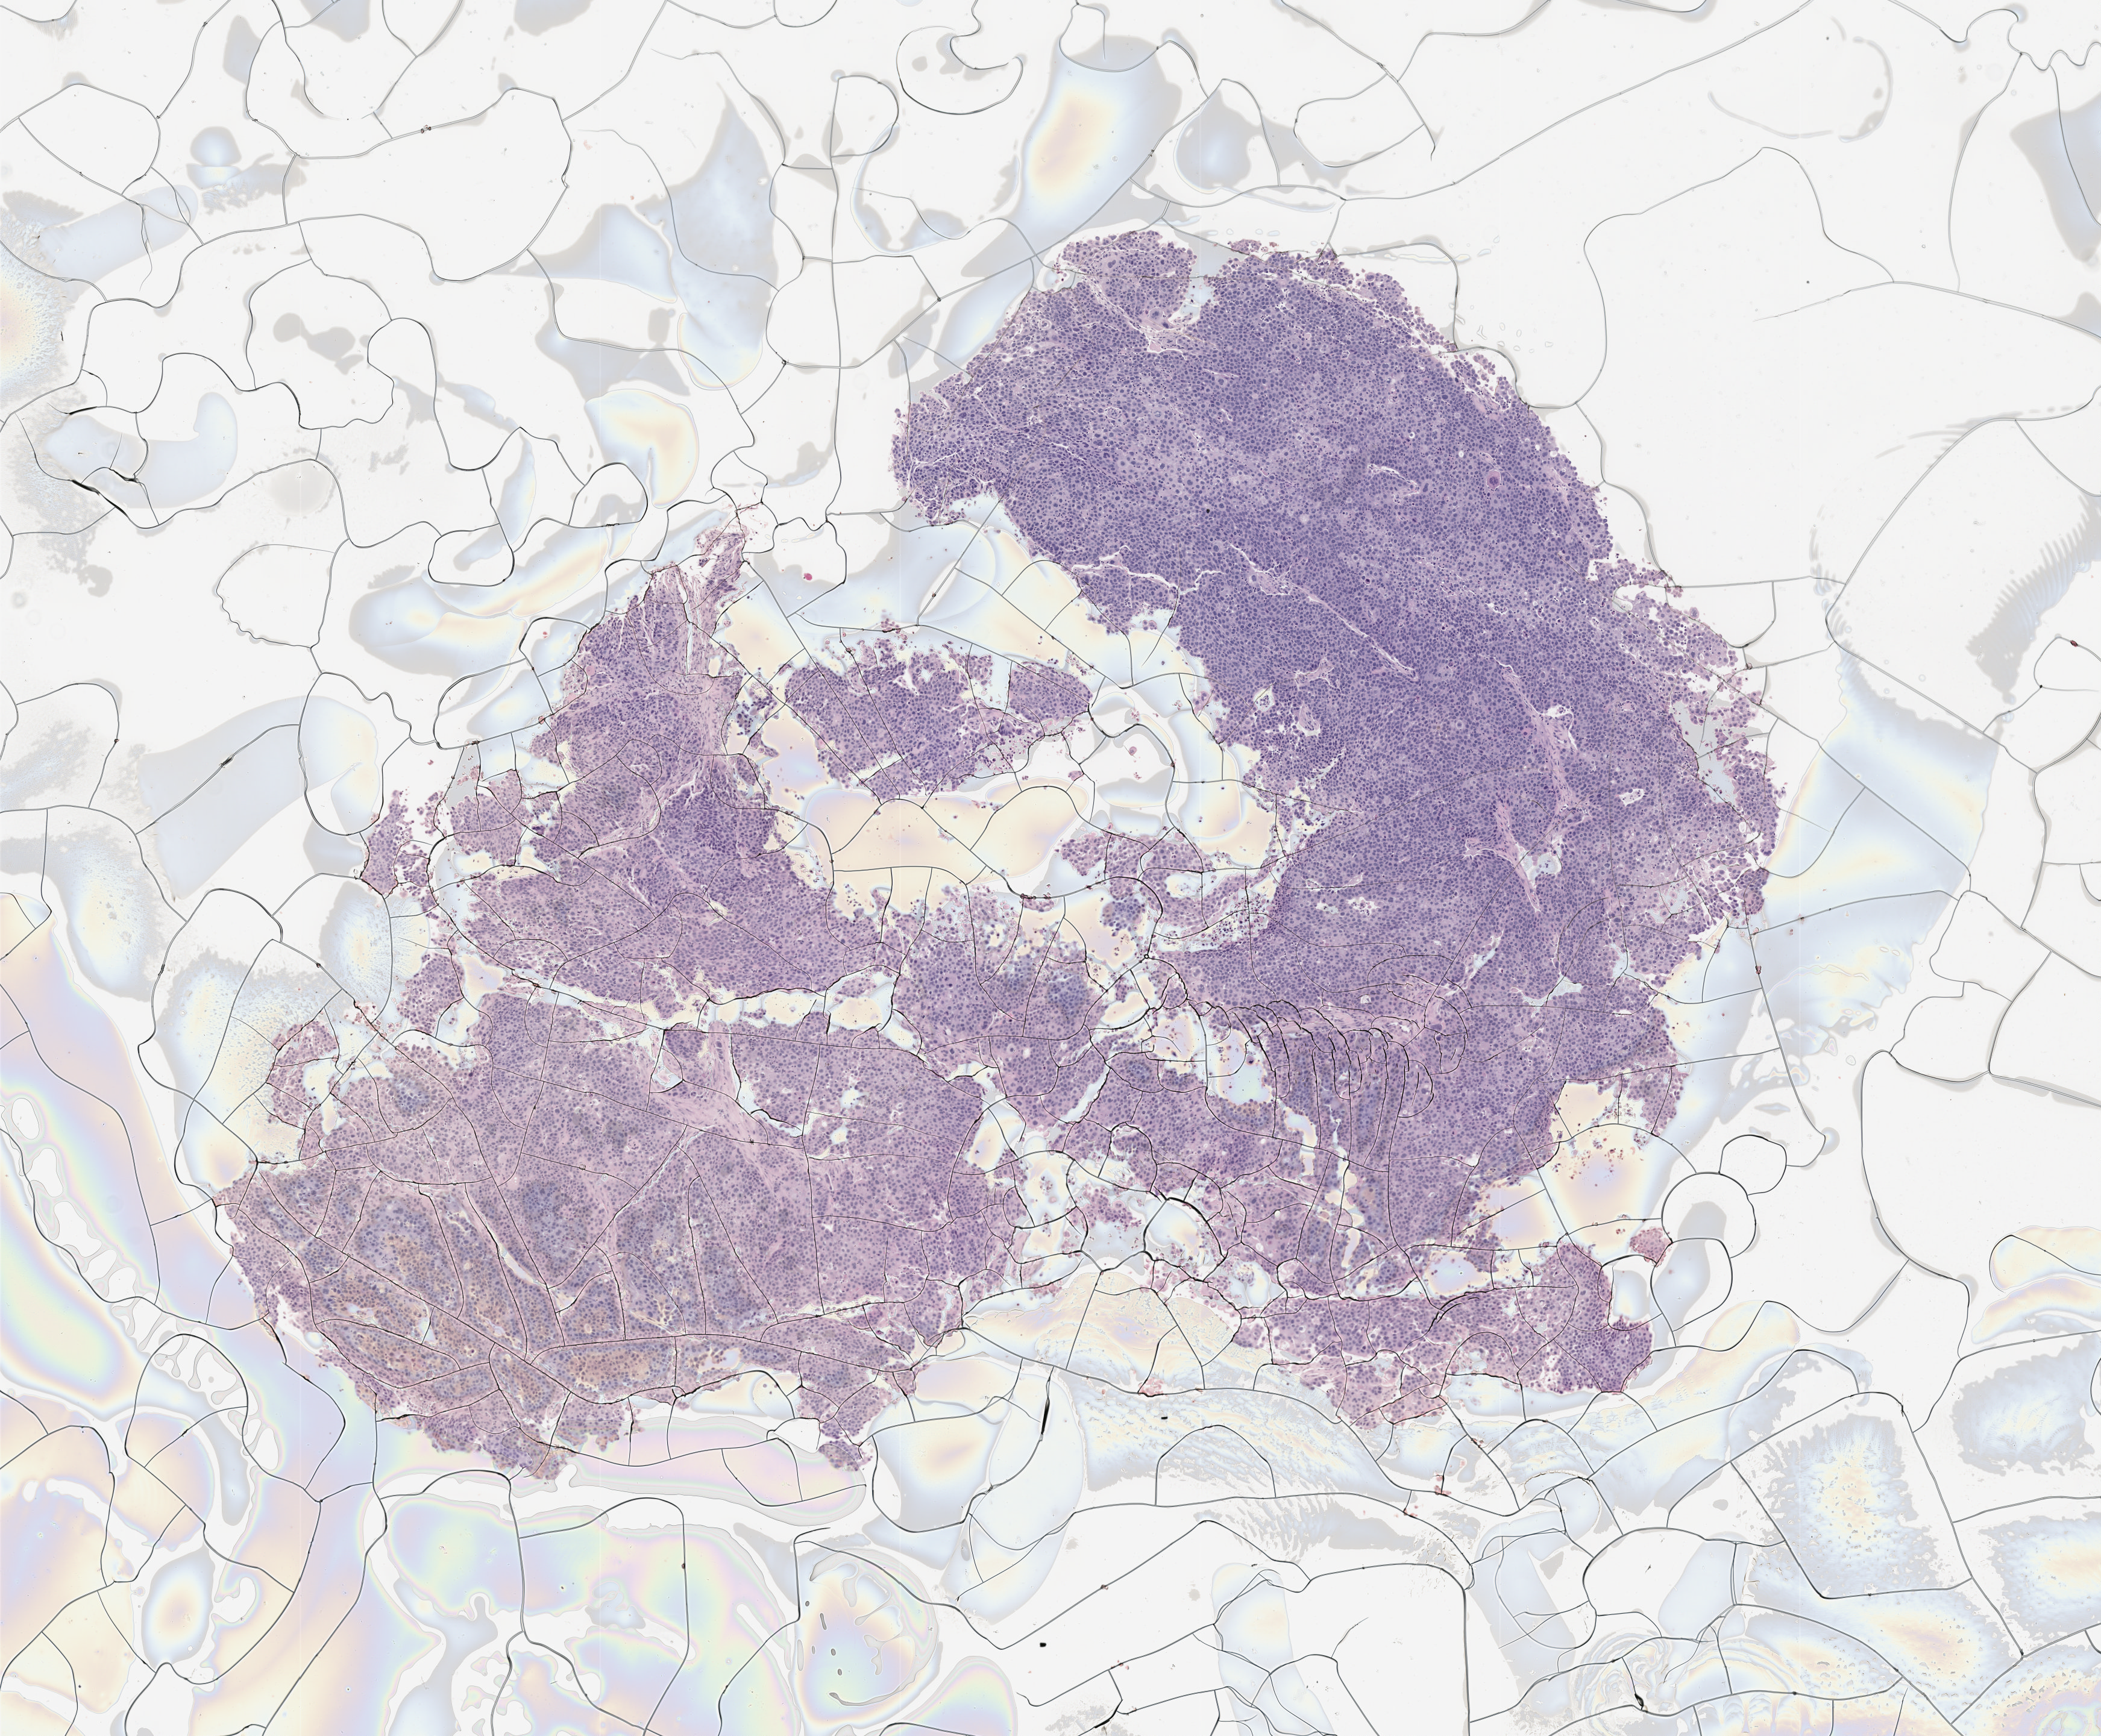
Haematoxylin and eosin whole-slide image of a patient-derived xenograft (PDX) tumor grown in a mouse, passage 2 — whole scanned area (about 7.0 x 5.8 mm) shown as a low-resolution overview. Formalin-fixed paraffin-embedded section. Tumor site category: bladder.
Originating patient diagnosis: Urothelial Carcinoma.